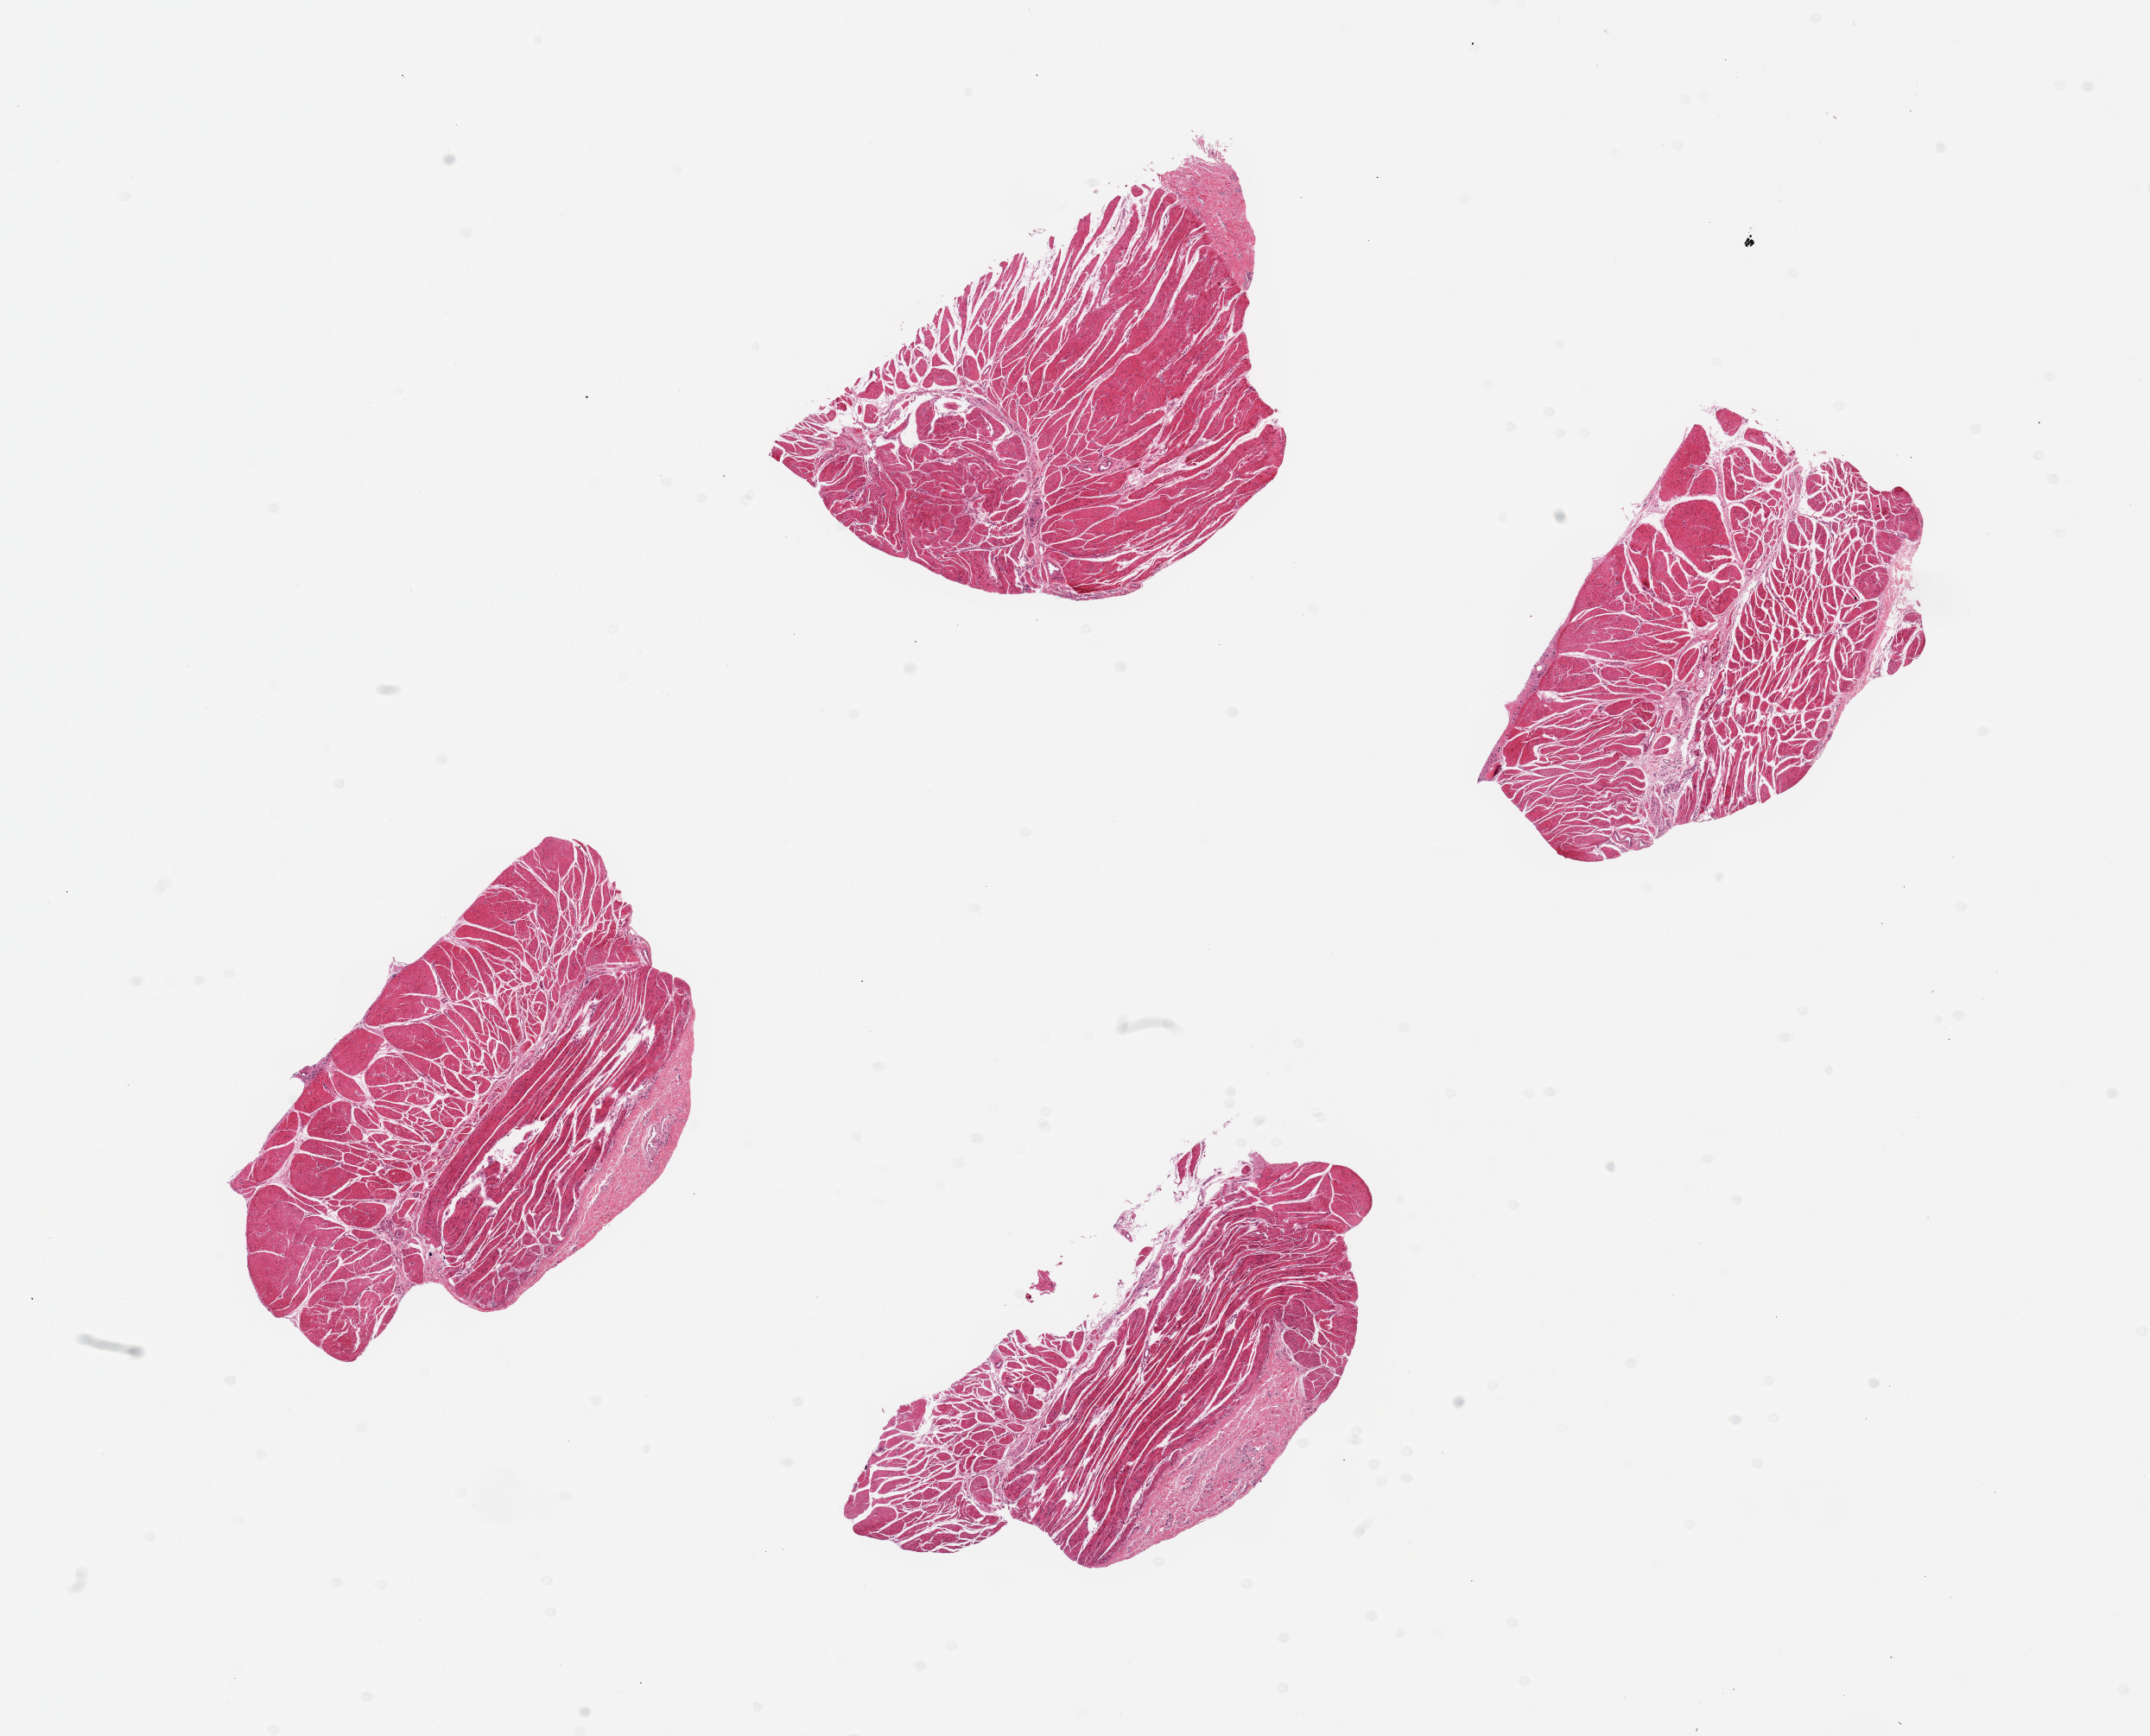
Digitized H&E-stained section — a low-resolution overview of the entire scanned area, about 19.7 x 15.9 mm (acquisition: 20x scan); PAXgene-fixed, paraffin-embedded tissue; section of esophageal muscle (target tissue); donor tissue sample. Donor: male.
Pathologist's review note for this sample: 4 pieces, up to 6x3mm; 2 have 10-20% fibrous stroma.